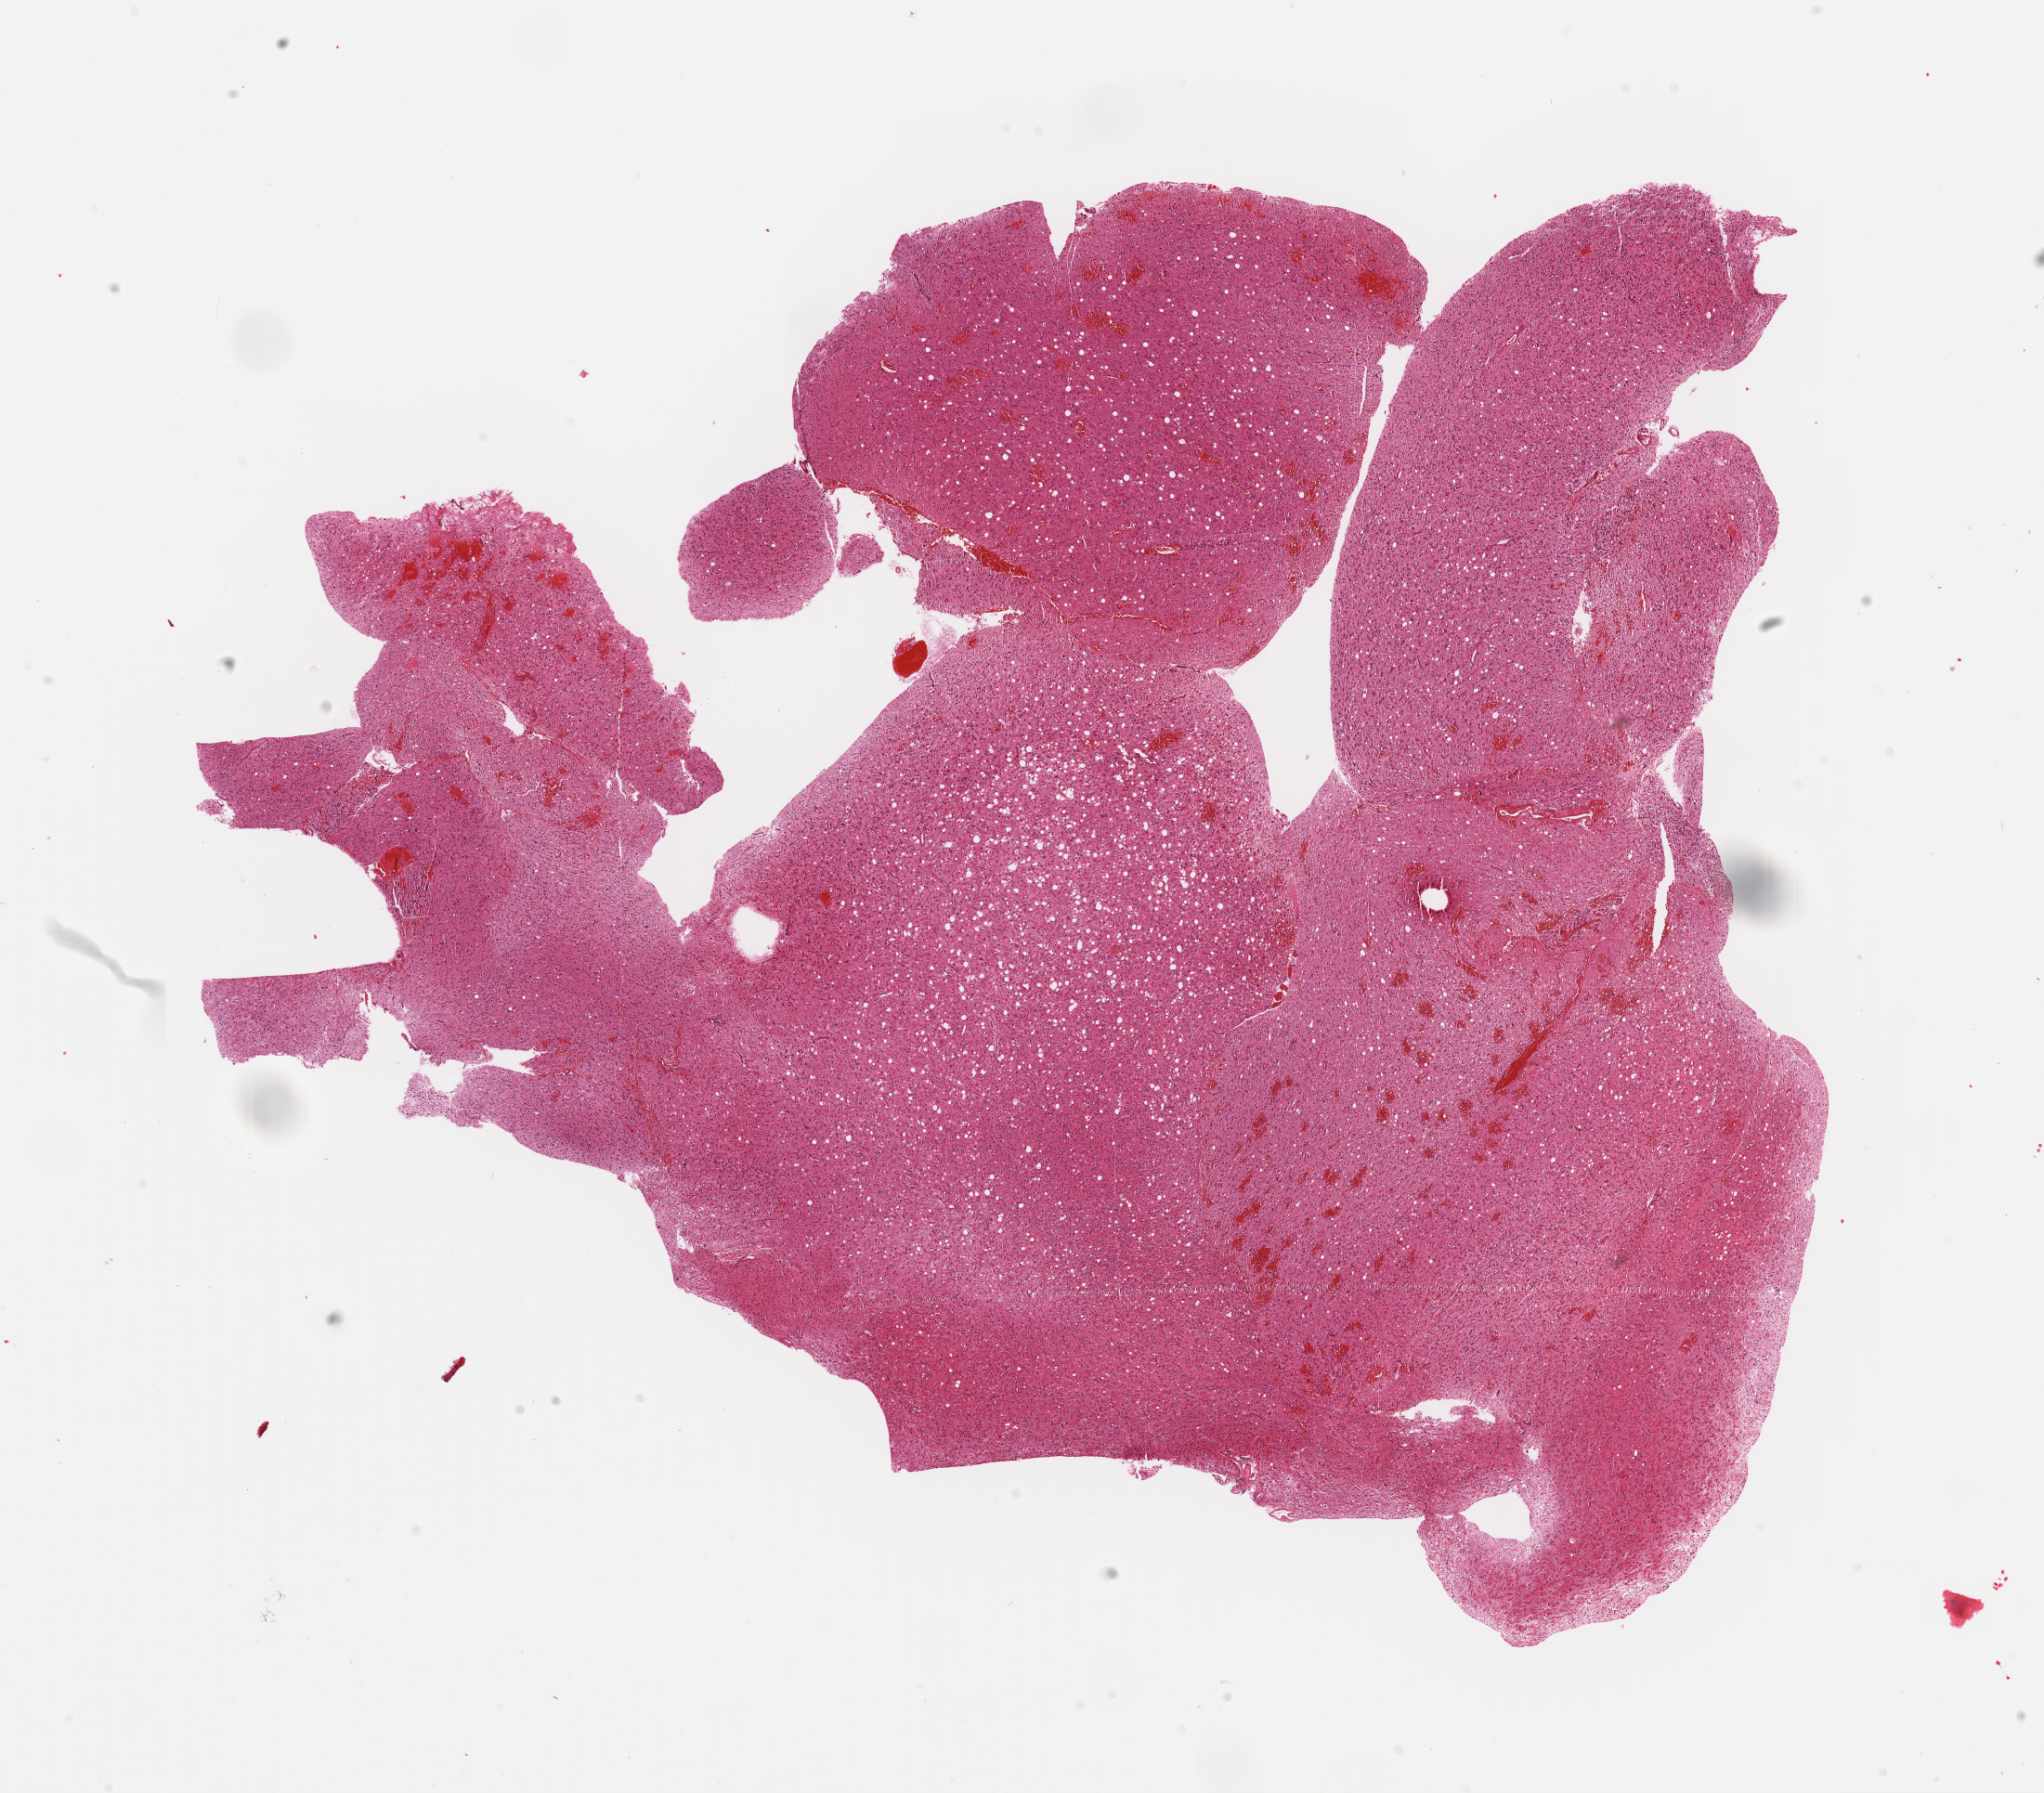
H&E whole-slide image — low-resolution overview of the scanned area, about 17.4 x 15.3 mm. Formalin-fixed paraffin-embedded (FFPE) diagnostic section. Brain, primary tumour sample. Male patient; age at initial diagnosis 63 years.
Histologic diagnosis: Mixed glioma (frontal lobe).